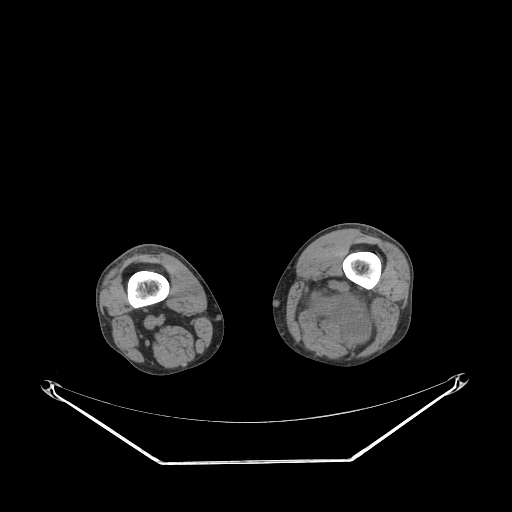
CT of an extremity soft-tissue mass (from a PET/CT study), one axial slice; position 204 of 267 along the scan axis; reconstruction kernel STANDARD; 140 kVp; soft-tissue window (W 400 / L 40 HU); 512 × 512 image matrix. Male patient. From the clinical record (not read from this slice): histological type: undifferentiated pleomorphic liposarcoma; grade: high; site of the primary tumour: left thigh.
Annotated regions visible in this slice (expert contour drawn on MRI and transferred to this co-registered scan by the dataset authors):
- gross tumour volume including surrounding oedema: box from (x=295, y=276) to (x=376, y=353) px